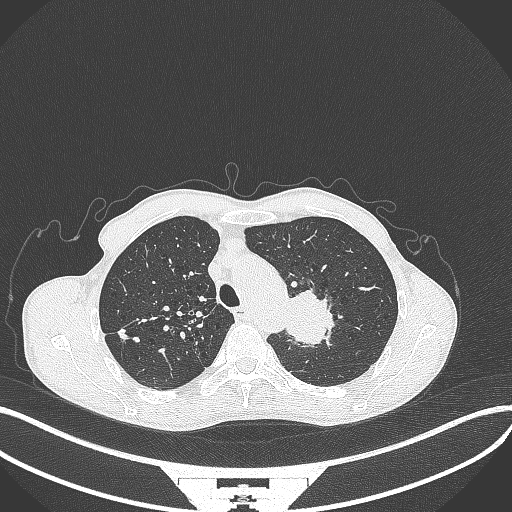
Chest CT, one axial slice. Position 323 of 386 along the scan axis. Reconstruction kernel B70f. 120 kVp. Lung window (W 1500 / L -600 HU). 1 mm slice thickness. 512 × 512 image matrix, field of view 400 × 400 mm. Patient: male, 65 years. Case-level facts recorded for this patient, not image findings: clinical TNM (as recorded): T2b N0 M0.
Structures marked on this image (bounding box drawn by a radiologist):
- lung tumour (recorded histology: adenocarcinoma): bounding box [x1, y1, x2, y2] px = [283, 284, 337, 350]